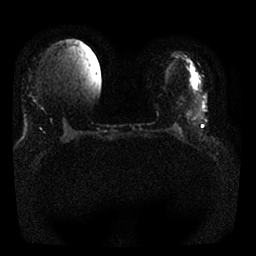
Breast MRI, one axial slice. Position 8 of 25 along the scan axis. Diffusion-weighted series; image 2 of 4 stored at this slice position (different b-values; order by instance number). 1.5 T. 4 mm slice thickness. 256 × 256 image matrix, field of view 320 × 320 mm. Female patient.
Outlined on this slice (expert manual segmentation):
- tumour on diffusion-weighted imaging: box from (x=194, y=81) to (x=197, y=88) px